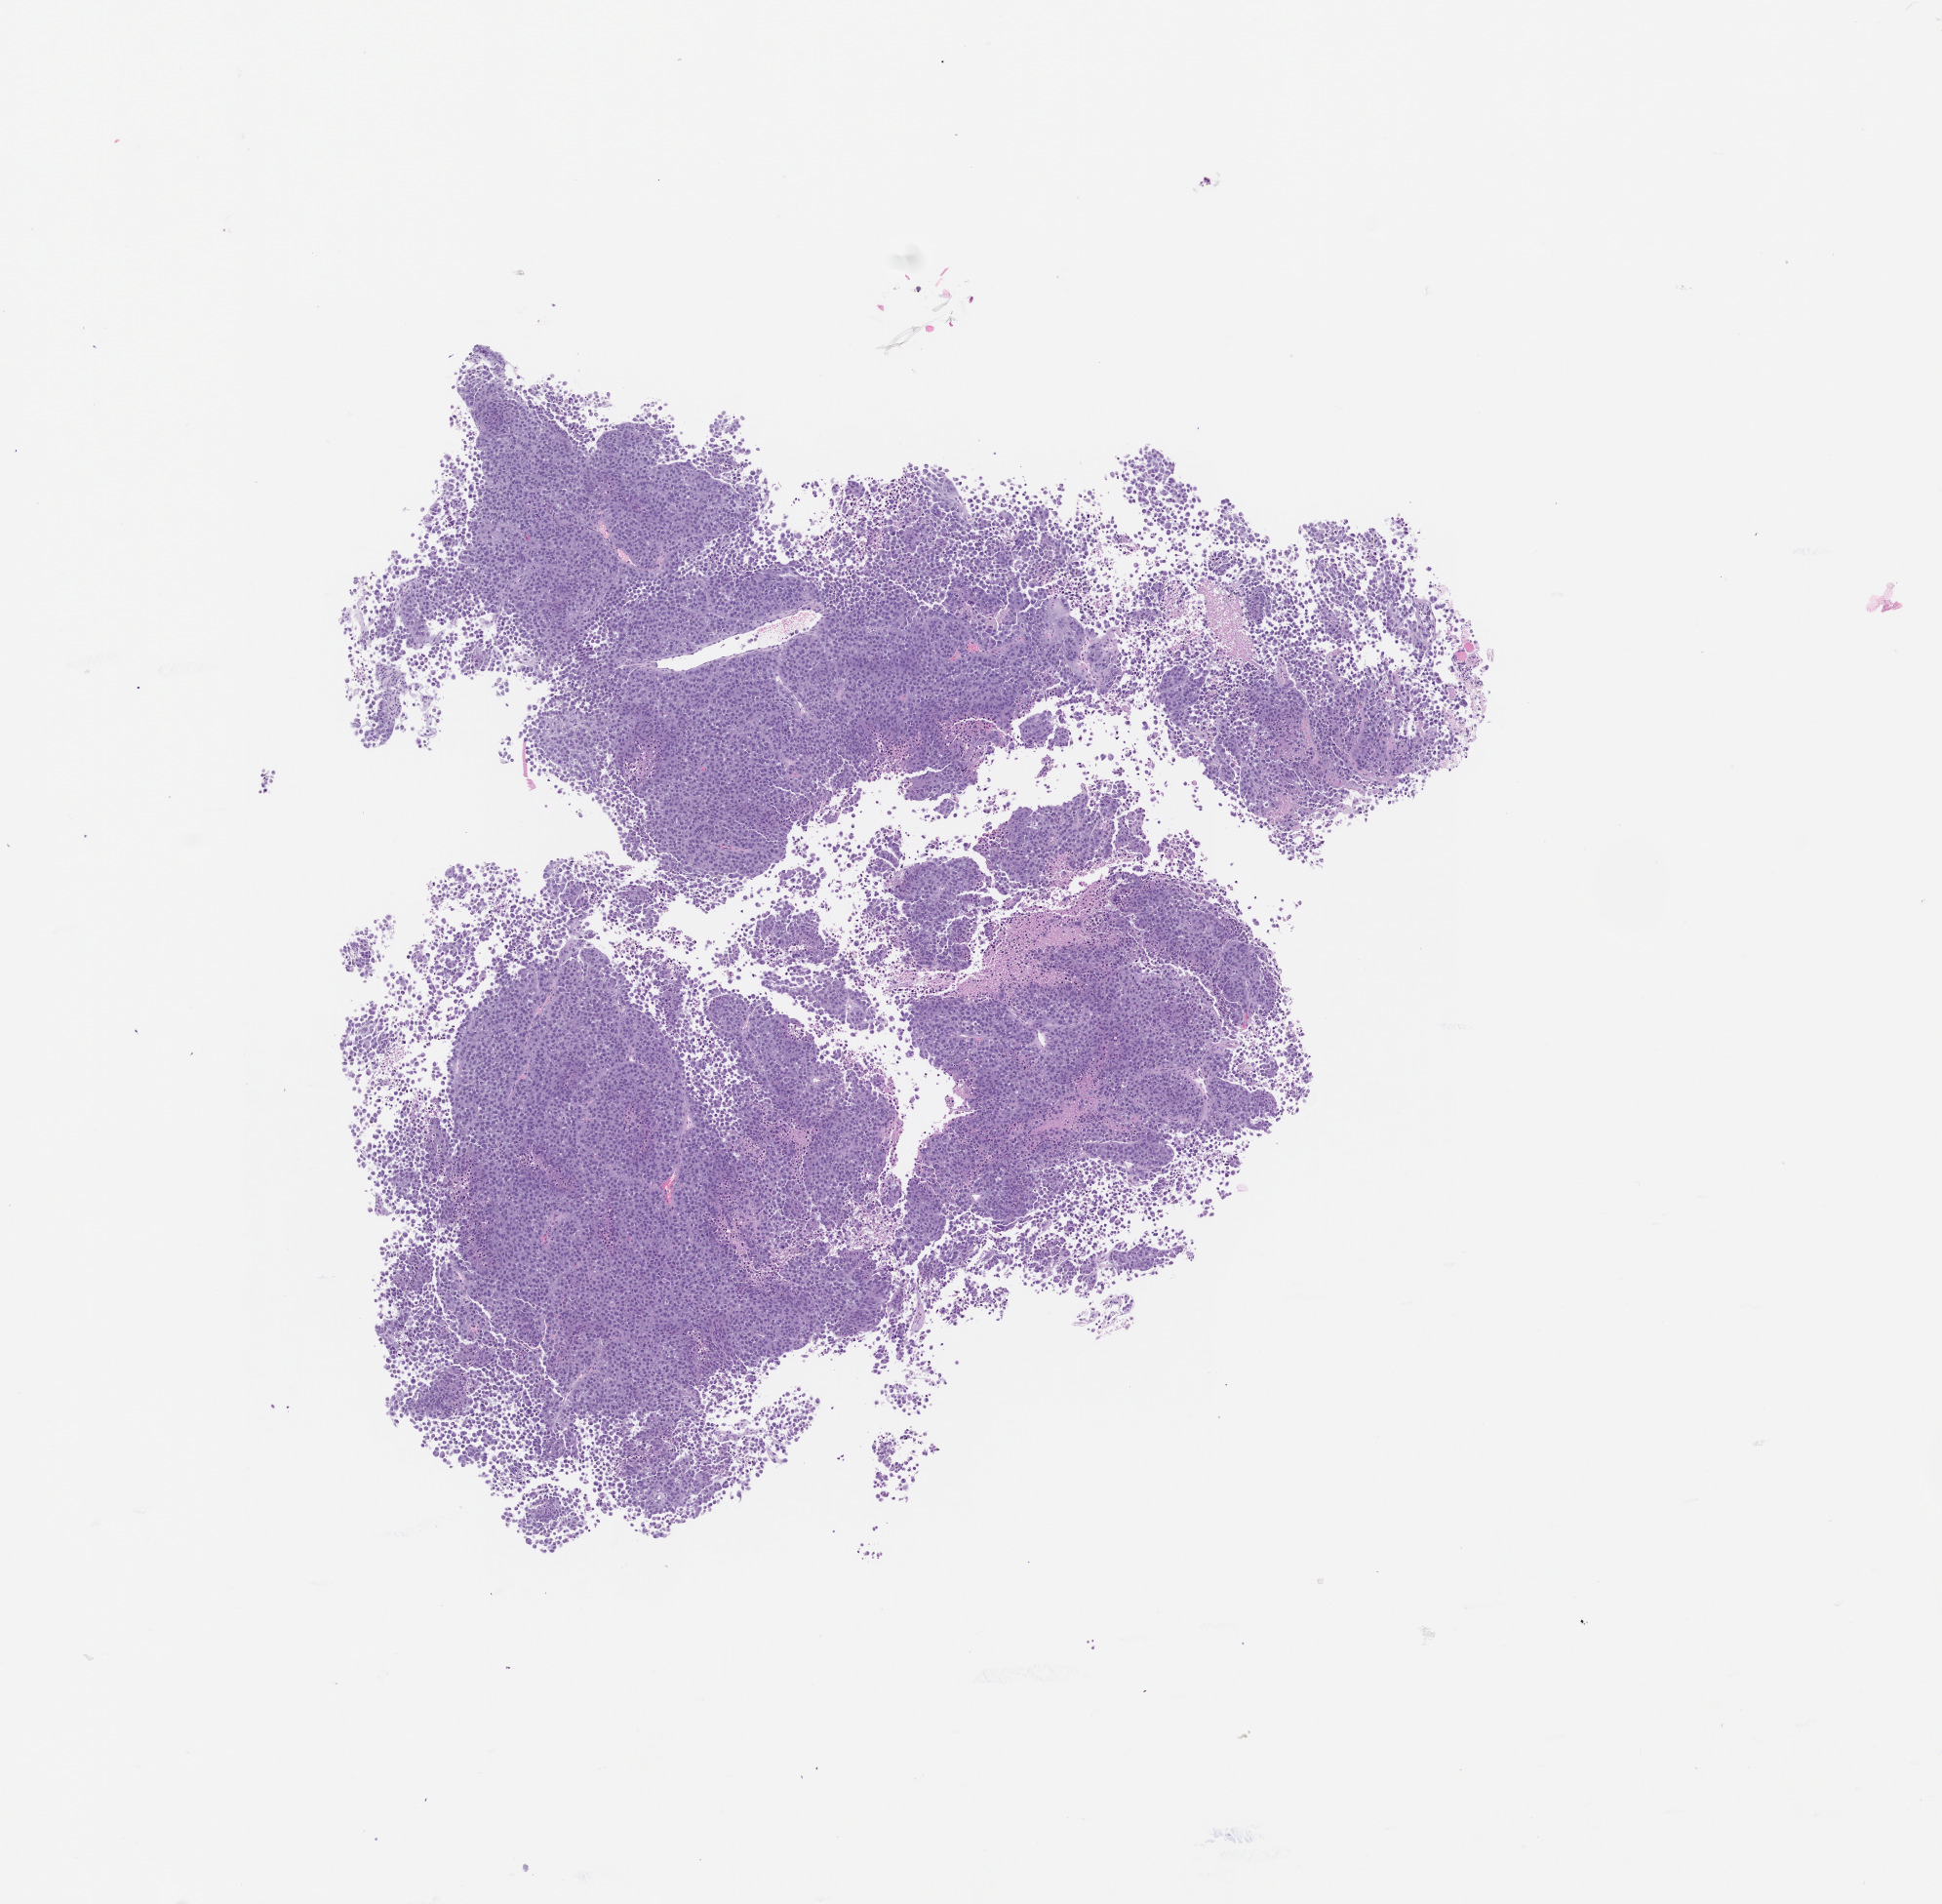
H&E whole-slide image of a patient-derived xenograft (PDX) tumor grown in a mouse, passage 3 — whole scanned area (about 8.0 x 7.8 mm) shown as a low-resolution overview. Formalin-fixed paraffin-embedded section. Tumor site category: skin.
Originating patient diagnosis: Melanoma.